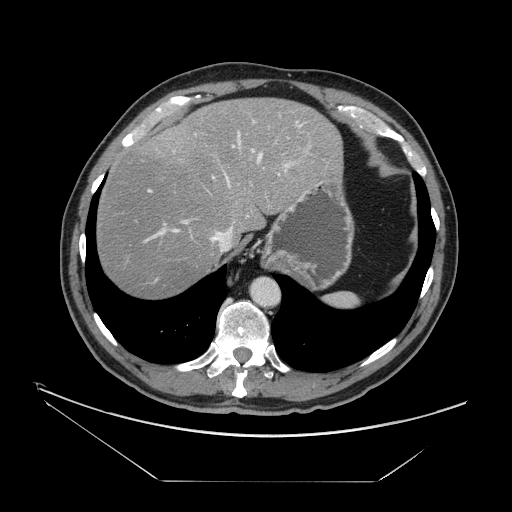
Contrast-enhanced abdominal CT, one axial slice; slice 125 of 161 in the series (ordered by position); reconstruction kernel STANDARD; soft-tissue window (W 400 / L 40 HU); 2.5 mm slice thickness; 512 × 512 image matrix, field of view 440 × 440 mm. Male patient, age 65 years. Case-level facts recorded for this patient, not image findings: diagnosis: colorectal cancer liver metastases, imaged before liver resection; multiple liver metastases: yes; largest metastasis: 4.2 cm; disease in both lobes: yes.
Annotated regions visible in this slice (expert manual segmentation):
- hepatic veins: bounding box (x1, y1, x2, y2) in pixels: (172, 130, 279, 251)
- liver: (96, 98, 342, 298)
- planned liver remnant (the part of the liver to remain after resection): (96, 98, 342, 299)
- portal vein (with intrahepatic branches): (148, 113, 306, 240)